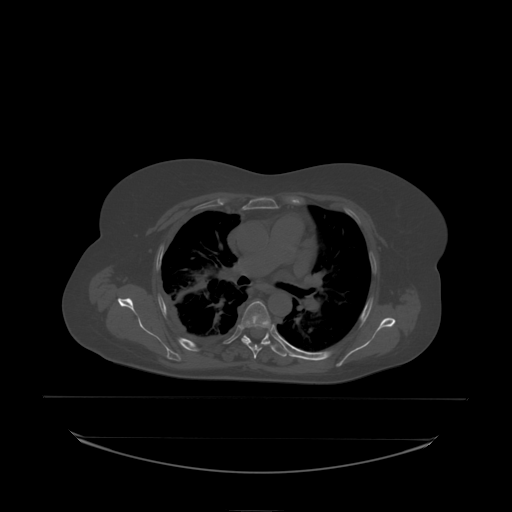
CT including the spine, one axial slice. Position 155 of 242 along the scan axis. Bone window (W 1800 / L 400 HU). 2.5 mm slice thickness. 512 × 512 image matrix. Patient: female, 53 years. From the clinical record (not read from this slice): primary cancer: lung.
Structures marked on this image (semi-automatic segmentation, software-assisted and operator-edited):
- T5 vertebra: bounding box [x1, y1, x2, y2] px = [243, 301, 269, 327]
- T6 vertebra: [241, 317, 272, 338]